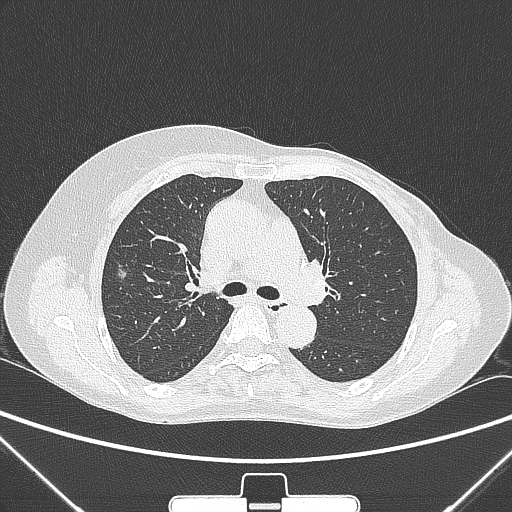
Chest CT, one axial slice. Slice 163 of 265 in the series (ordered by position). 120 kVp. Lung window (W 1500 / L -600 HU). 1 mm slice thickness. 512 × 512 image matrix. Female patient, age 64 years. Case-level facts recorded for this patient, not image findings: clinical TNM (as recorded): T1c N0 M0; histopathological grade: G1-2.
Structures marked on this image (rectangle marked by the reading radiologist):
- lung tumour (recorded histology: adenocarcinoma): bounding box <113,263,129,279> (left, top, right, bottom; pixels)